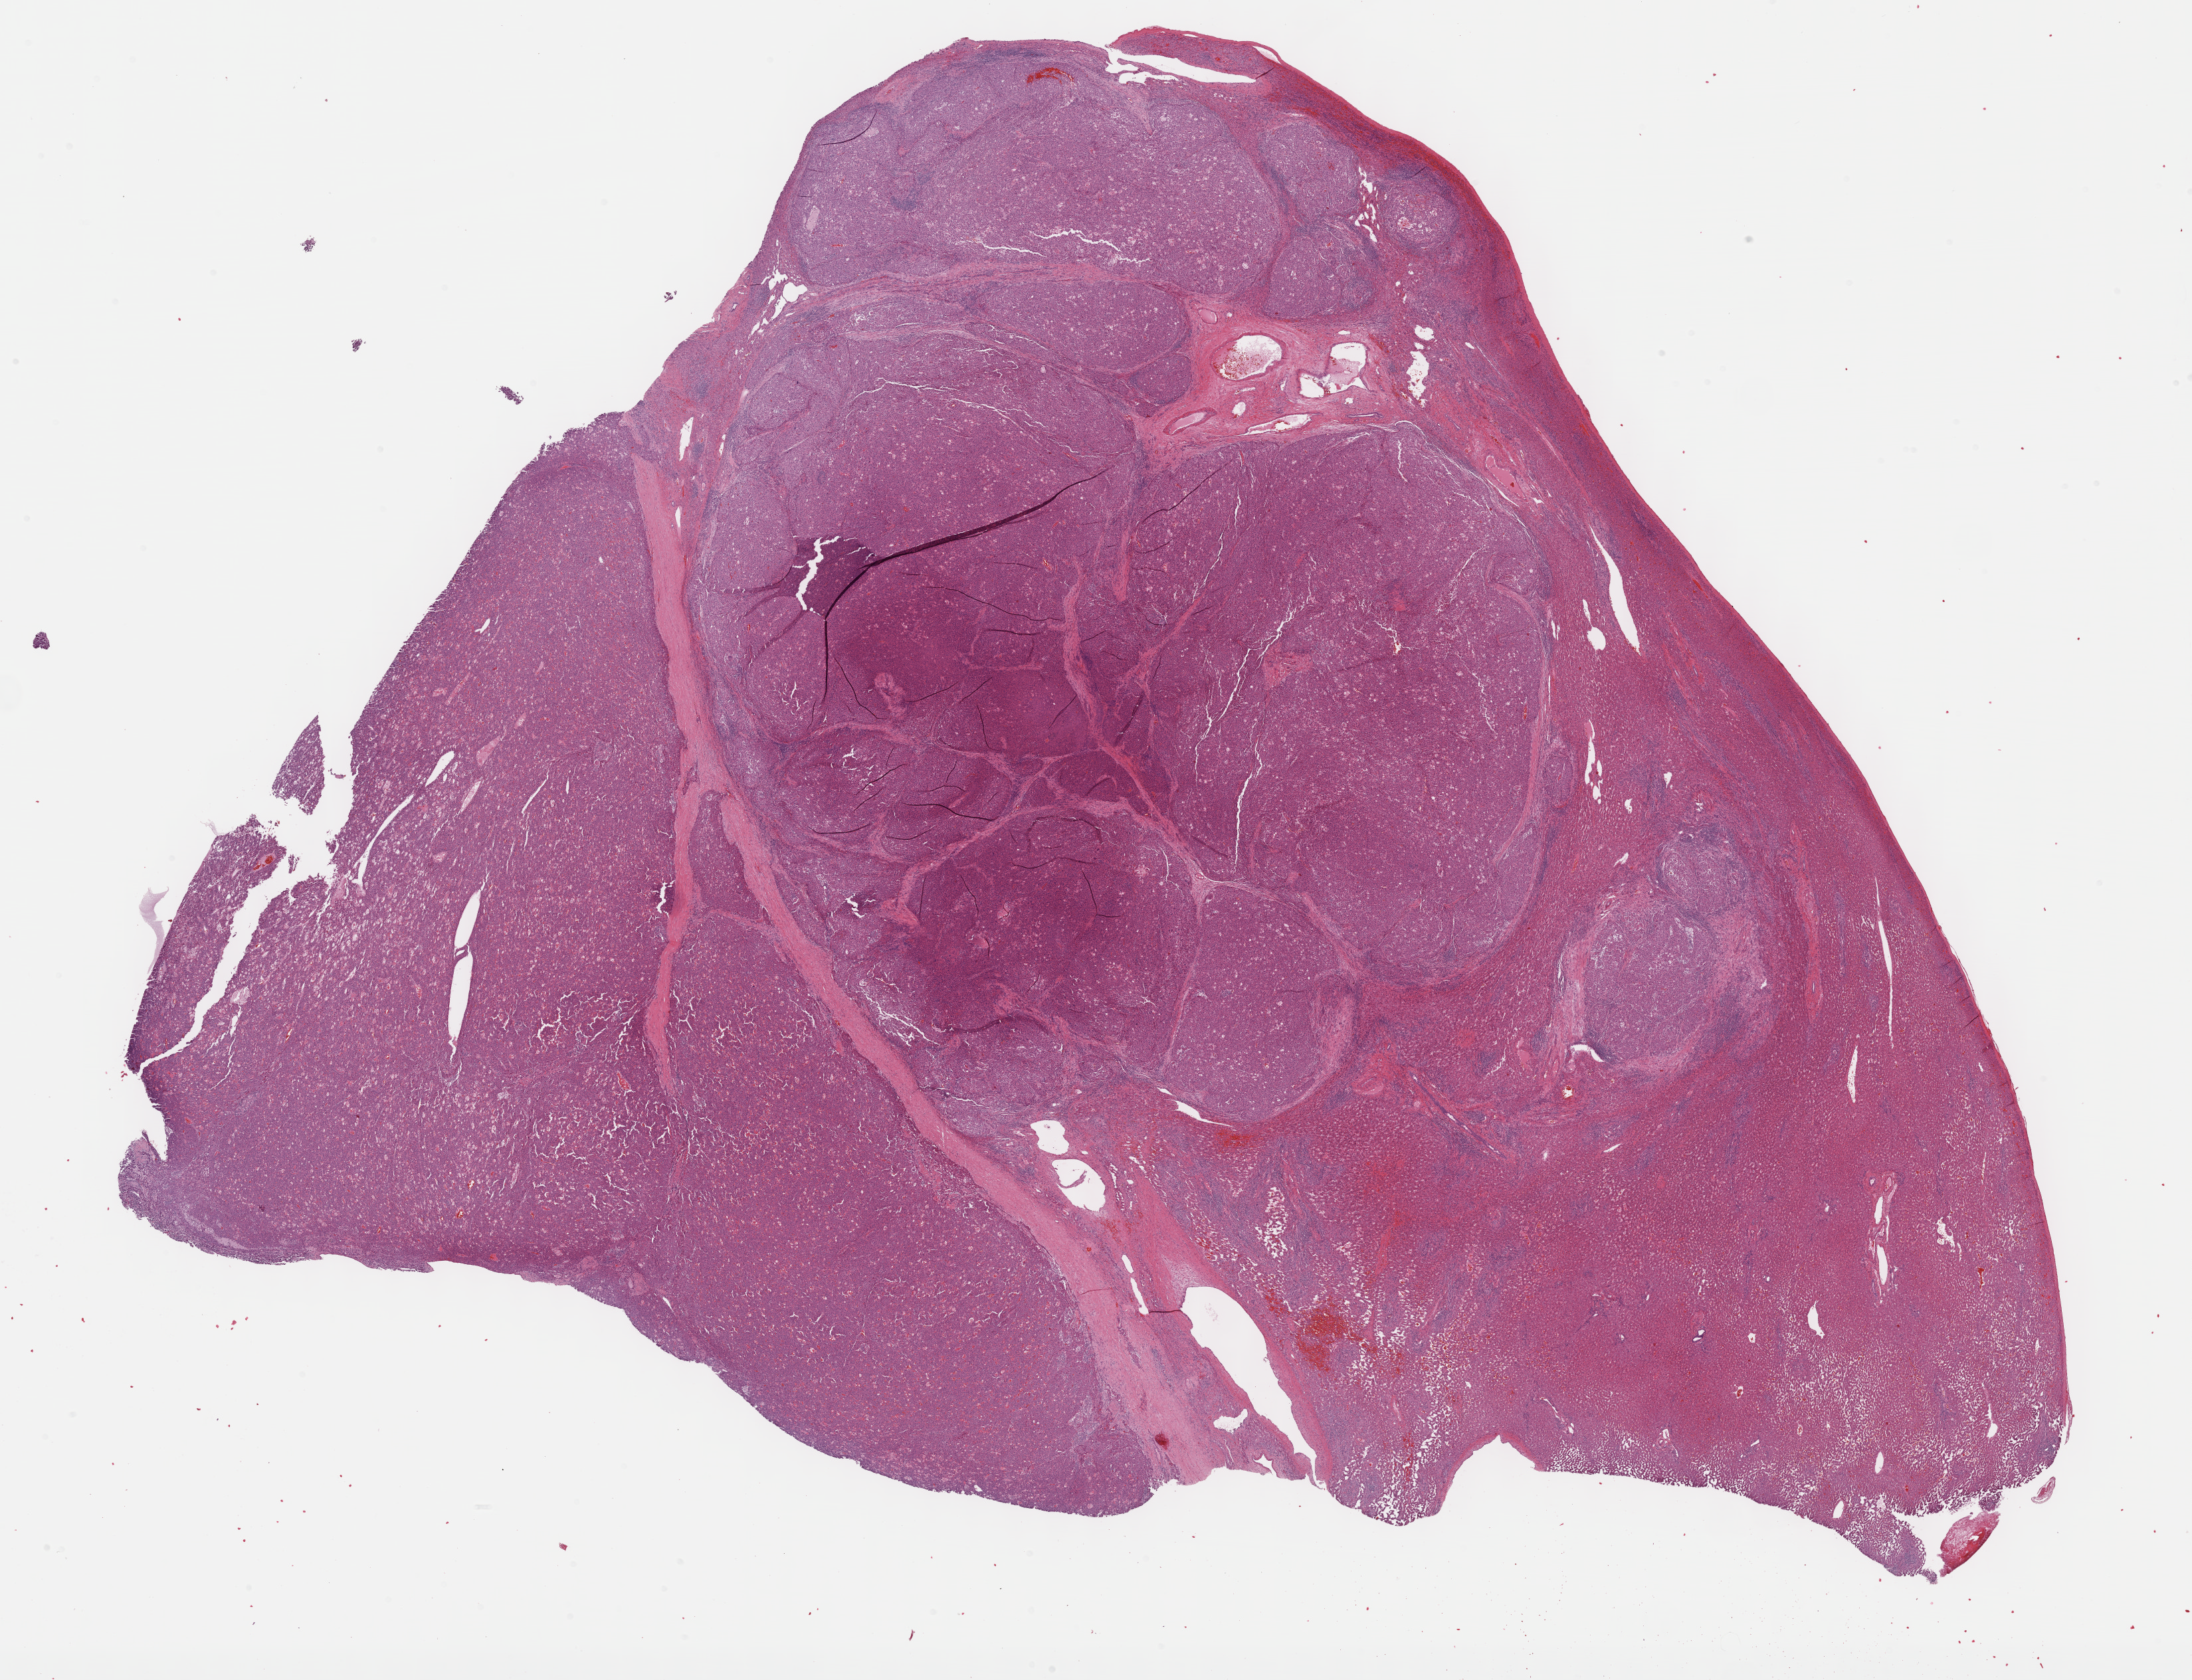
Digitized H&E-stained tissue section (whole slide) — a low-resolution overview of the entire scanned area, about 26.7 x 20.5 mm; FFPE section; liver, primary tumour sample. Female patient; age at initial diagnosis 20 years. Histologic grade: G3 (poorly differentiated).
AJCC pathologic stage: I. Pathologic diagnosis: Hepatocellular carcinoma, NOS.